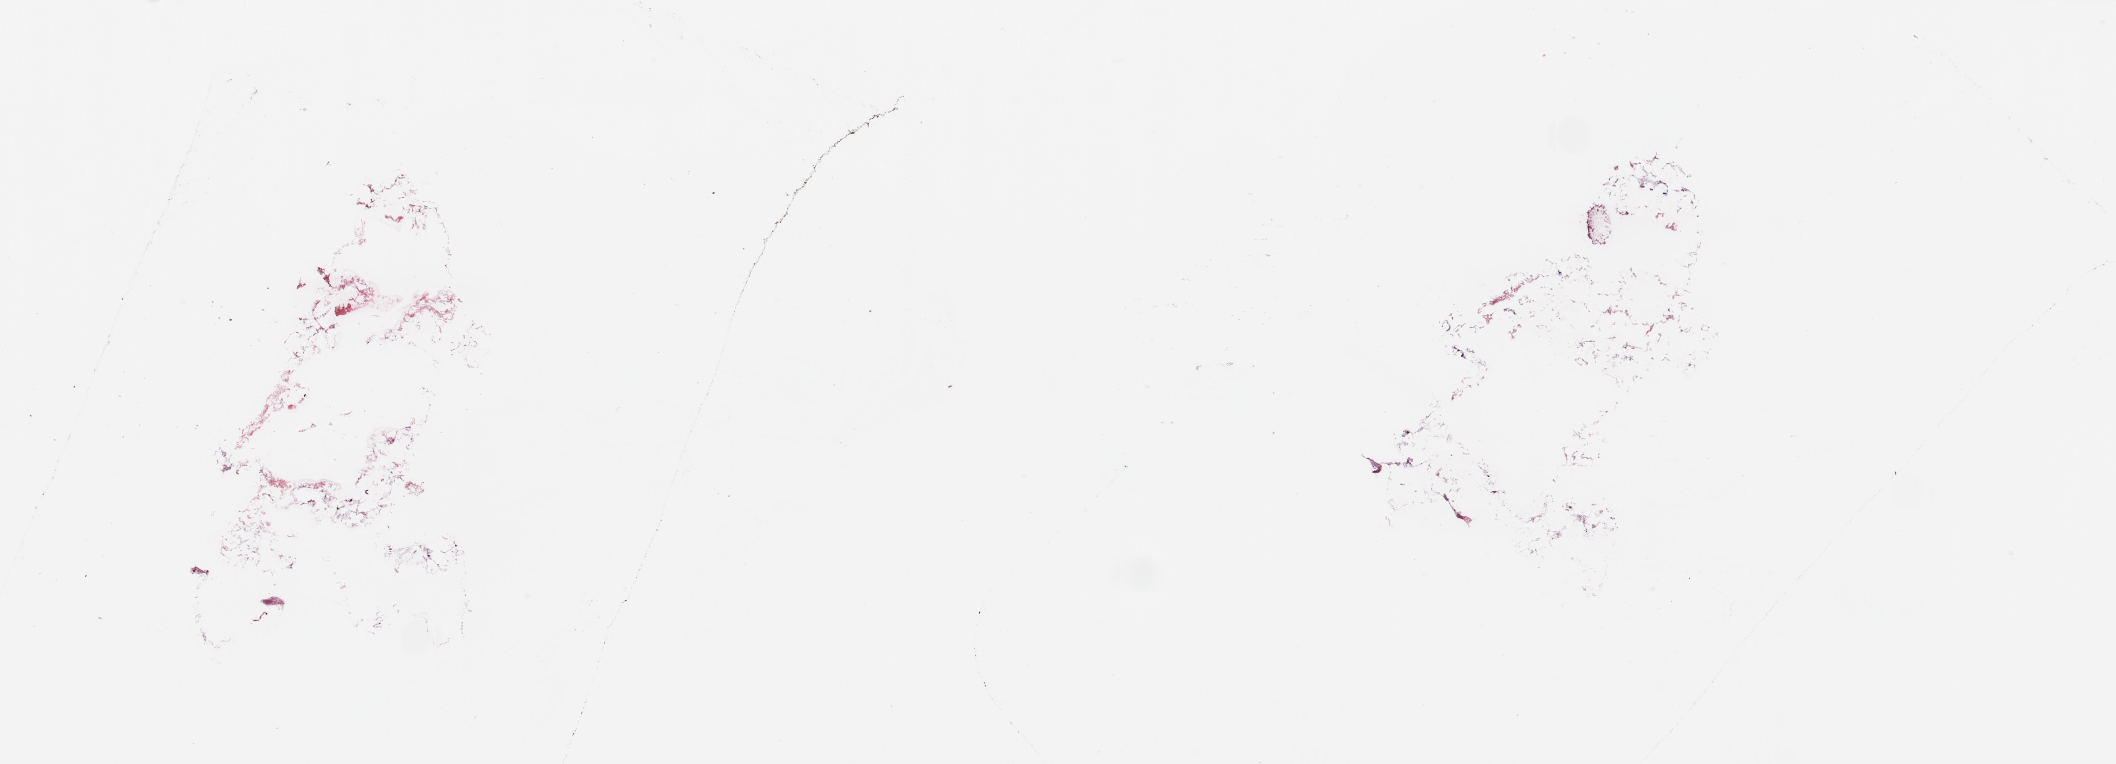
H&E whole-slide image — a low-resolution overview of the entire scanned area, about 33.5 x 12.1 mm; tumour tissue sample, breast. Female, 59 y/o.
AJCC pathologic stage: II. Diagnosis: Adenocarcinoma, NOS.